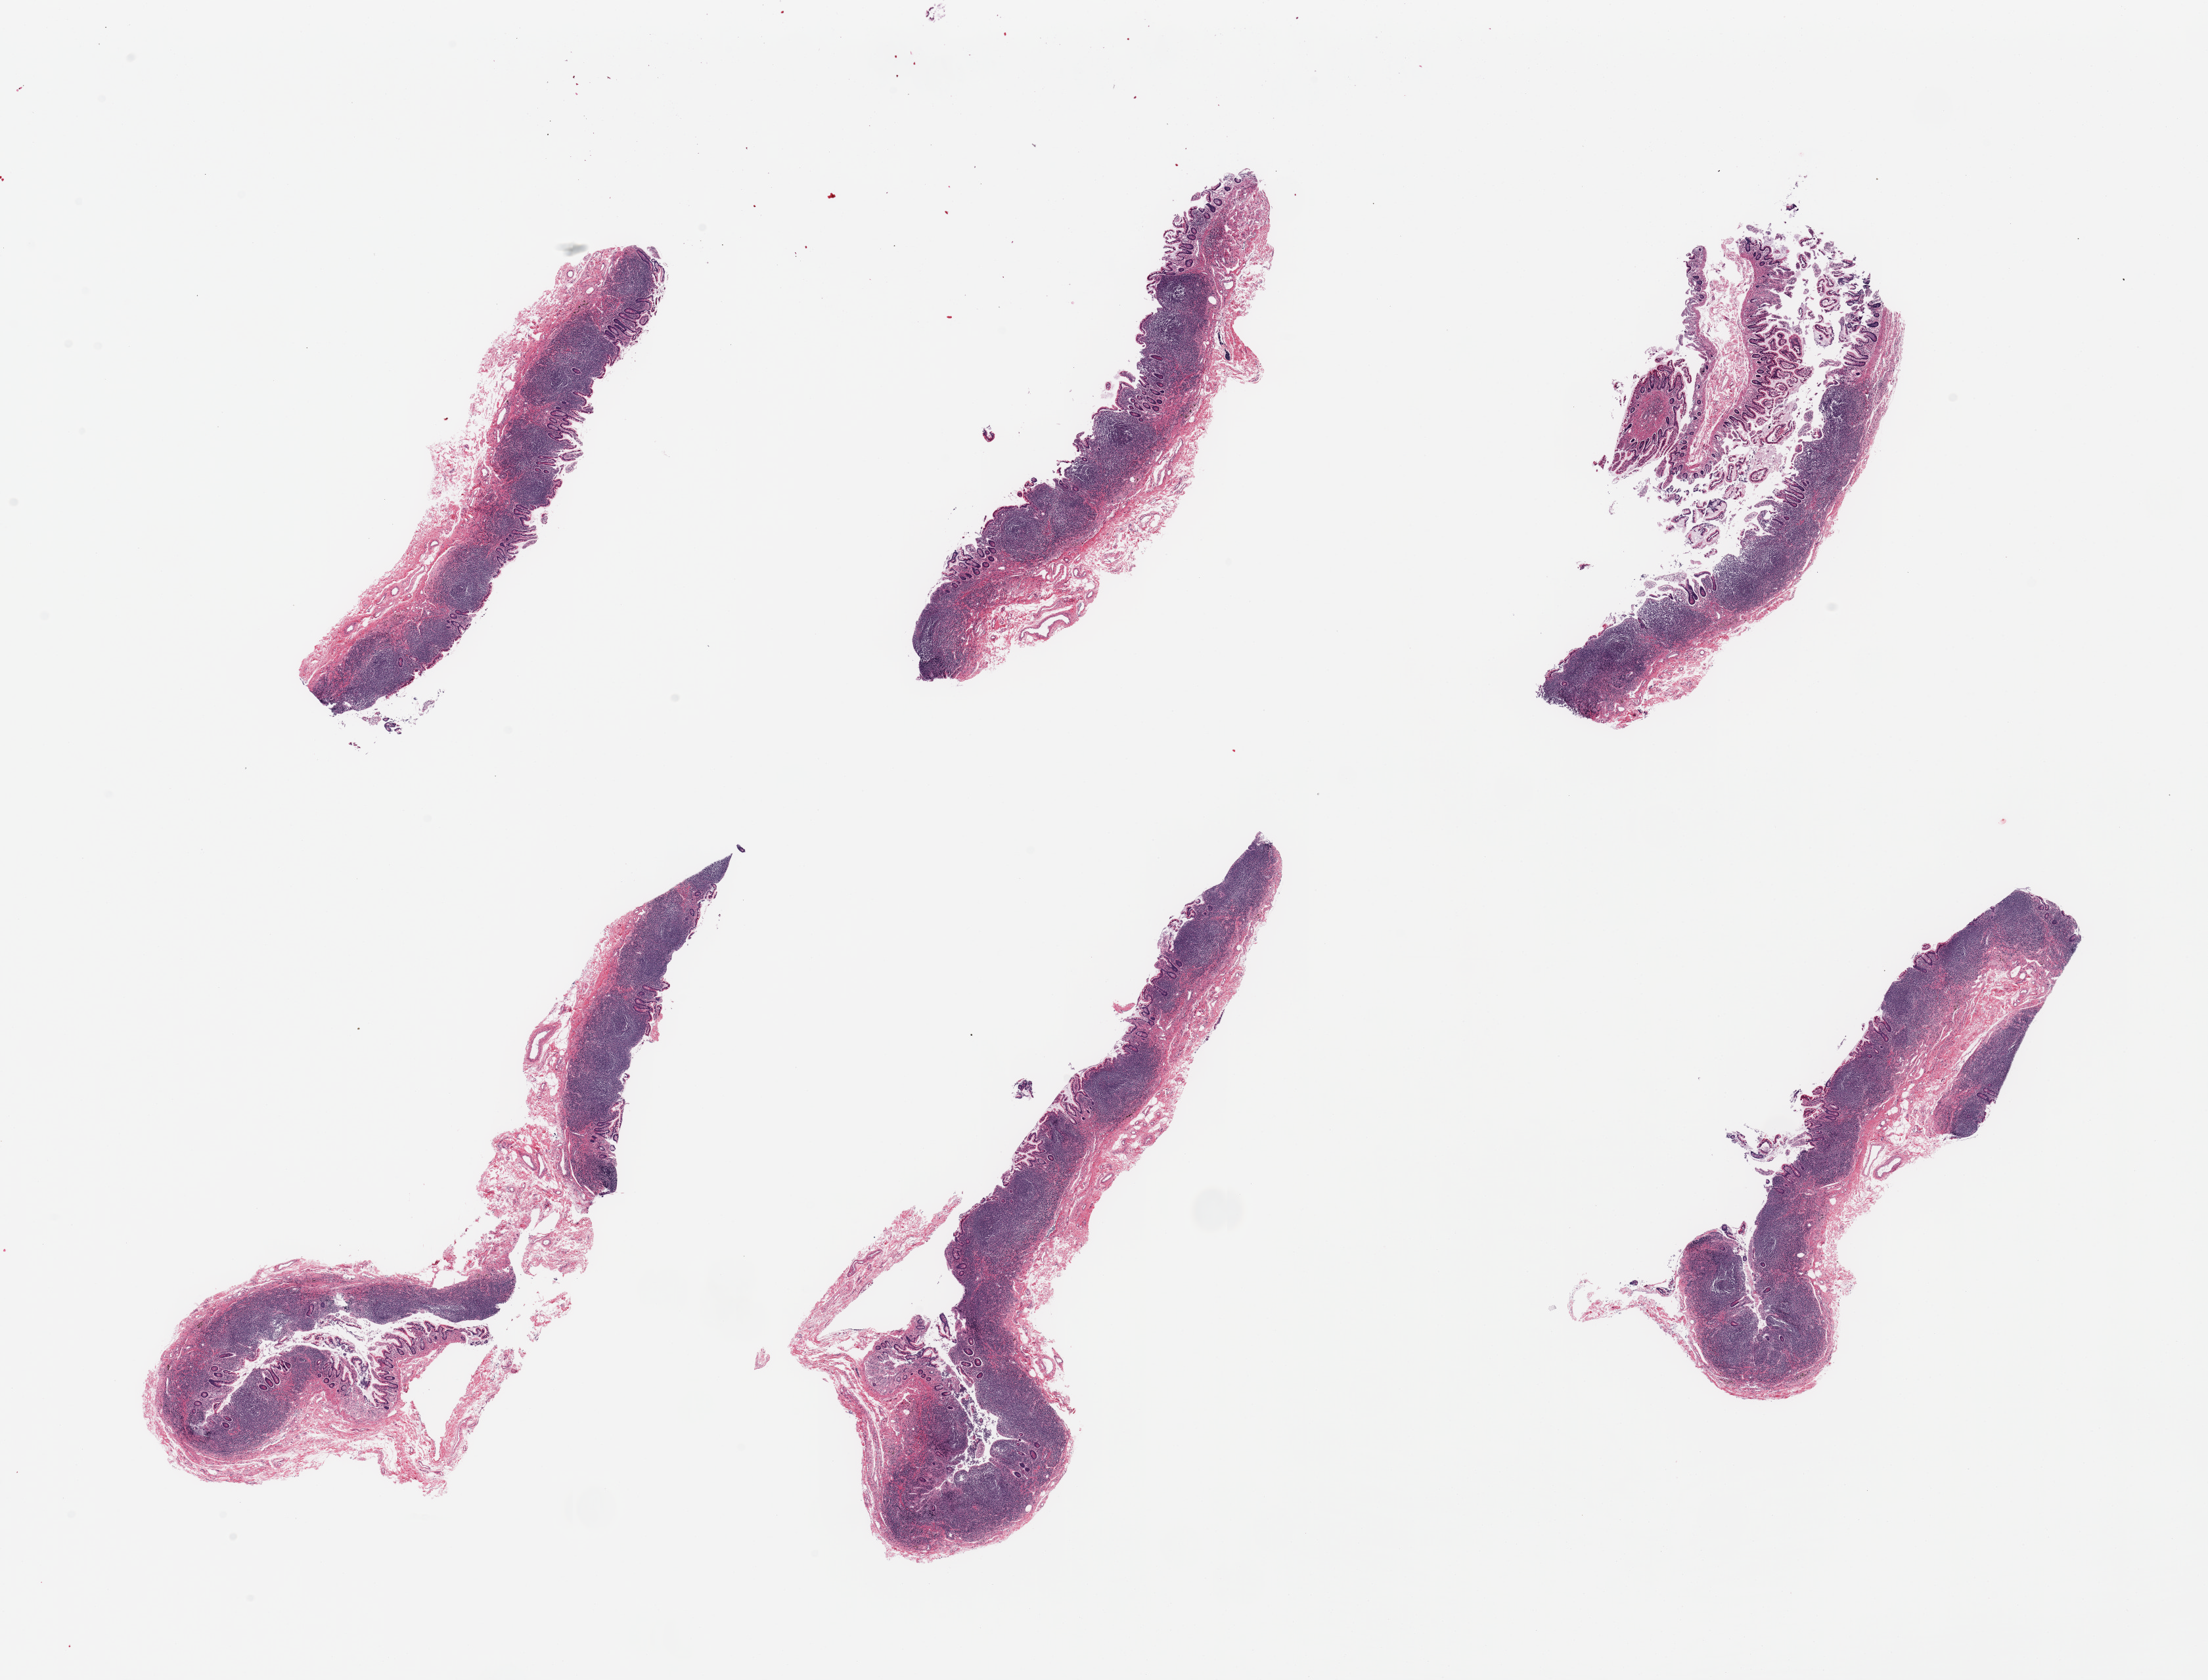
Whole-slide image, haematoxylin and eosin stain — low-resolution overview of the scanned area, about 26.6 x 20.2 mm (acquisition: 20x scan); PAXgene-fixed, paraffin-embedded tissue; sampled site (target tissue): ileum; donor tissue sample. Male donor.
* review note (as recorded): 6 pieces; well trimmed with significant lymphoid component